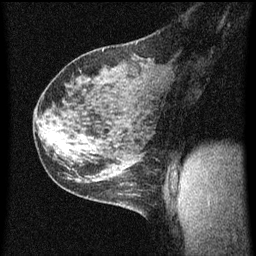
Breast MRI (dynamic contrast-enhanced), one sagittal slice. Slice 36 of 60 in the series (ordered by position). Dynamic contrast-enhanced series, image 2 of 3 at this slice position (ordered by acquisition). 1.5 T. TE 4.2 ms, TR 8 ms. 2 mm slice thickness. 256 × 256 image matrix, field of view 180 × 180 mm. Patient: female, 35 years.
Annotated regions visible in this slice (semi-automatic segmentation, software-assisted and operator-edited):
- analysis volume of interest (the breast-tissue region the enhancement analysis was run in; not a lesion): bounding box <106,182,145,217> (left, top, right, bottom; pixels)
- tumour enhancement mask (voxels above the 70 % enhancement threshold inside the analysis volume of interest): <120,184,133,187>